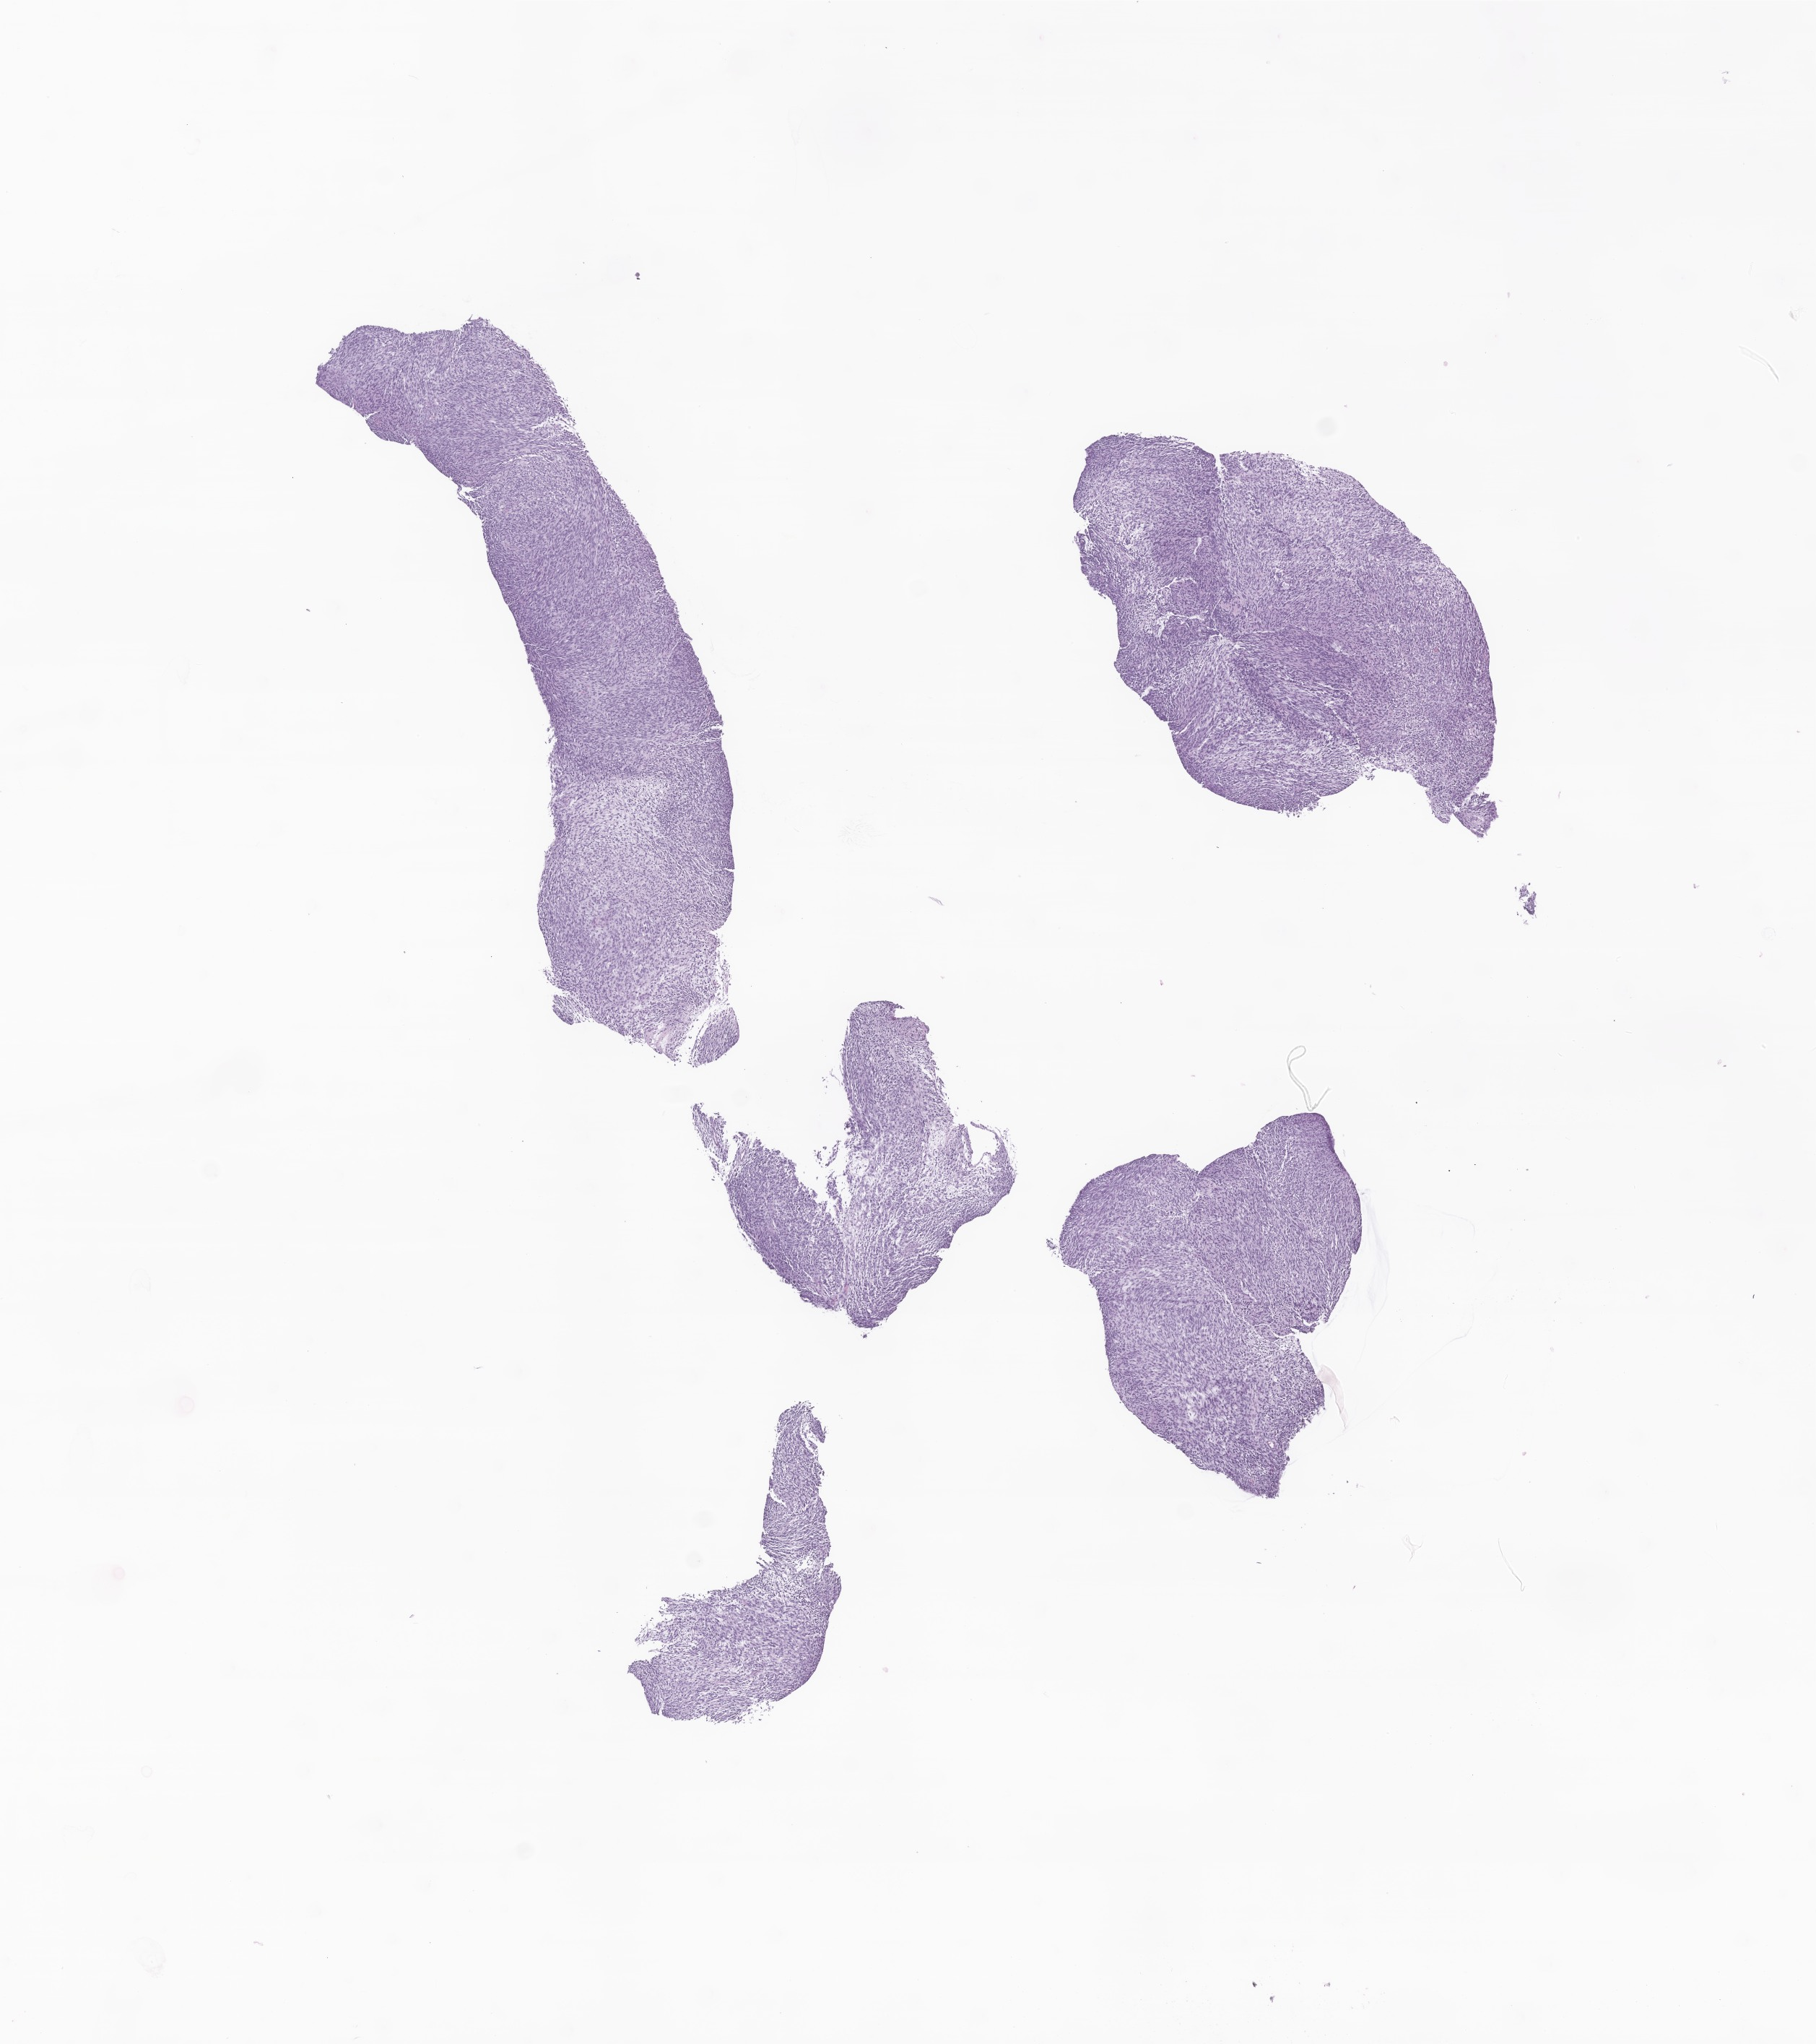
Digitized H&E-stained section of tumor tissue from the prostate, low-resolution overview of the scanned area, about 10.6 x 11.9 mm. Formalin-fixed paraffin-embedded section. Patient: male, age 379 days (about 1.0 years).
* diagnosis (ICD-O-3 morphology term): Embryonal rhabdomyosarcoma, NOS